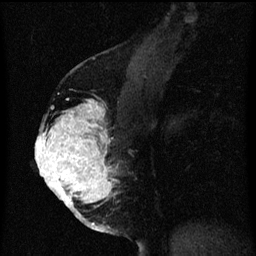
Breast MRI (dynamic contrast-enhanced), one sagittal slice. Slice 33 of 60 in the series (ordered by position). Dynamic contrast-enhanced series, image 2 of 3 at this slice position (ordered by acquisition). 1.5 T. TE 4.2 ms, TR 8 ms. 2 mm slice thickness. 256 × 256 image matrix, field of view 180 × 180 mm. Female patient, age 56 years.
Outlined on this slice (semi-automatic segmentation, software-assisted and operator-edited):
- analysis volume of interest (the breast-tissue region the enhancement analysis was run in; not a lesion): bounding box [x1, y1, x2, y2] px = [40, 100, 123, 209]
- tumour enhancement mask (voxels above the 70 % enhancement threshold inside the analysis volume of interest): [40, 100, 113, 207]